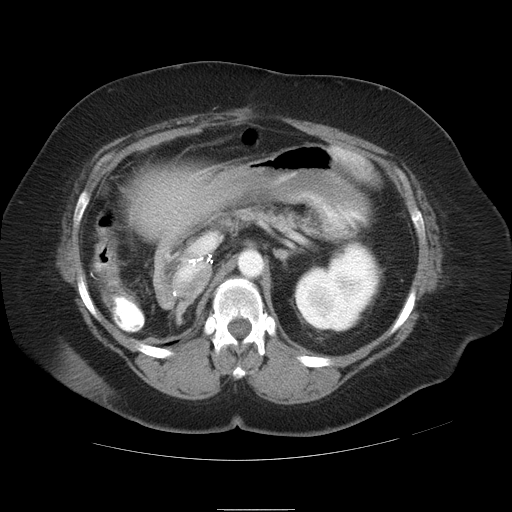
Contrast-enhanced abdominal CT, one axial slice; position 21 of 37 along the scan axis; reconstruction kernel STANDARD; 120 kVp; intravenous contrast given; soft-tissue window (W 400 / L 40 HU); 7.5 mm slice thickness; 512 × 512 image matrix, field of view 422 × 422 mm. Female patient, age 68 years. Case-level facts recorded for this patient, not image findings: diagnosis: colorectal cancer liver metastases, imaged before liver resection; multiple liver metastases: no; largest metastasis: 2 cm; chemotherapy before resection: no.
Structures marked on this image (outlined manually by an expert reader):
- liver: bounding box (x1, y1, x2, y2) in pixels: (128, 167, 252, 243)
- planned liver remnant (the part of the liver to remain after resection): (128, 167, 254, 243)